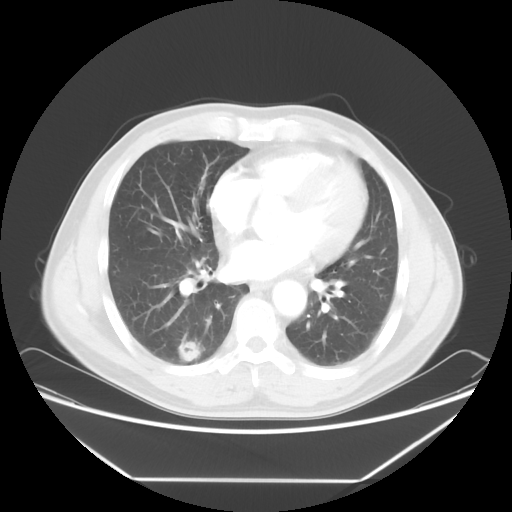
Chest CT, one axial slice; slice 30 of 65 in the series (ordered by position); reconstruction kernel STANDARD; lung window (W 1500 / L -600 HU); 5 mm slice thickness; 512 × 512 image matrix, field of view 418 × 418 mm. Patient: male, 50 years. From the clinical record (not read from this slice): clinical TNM (as recorded): T1c N0 M0.
Annotated regions visible in this slice (rectangle marked by the reading radiologist):
- lung tumour (recorded histology: adenocarcinoma): bounding box [x1, y1, x2, y2] px = [171, 337, 211, 365]